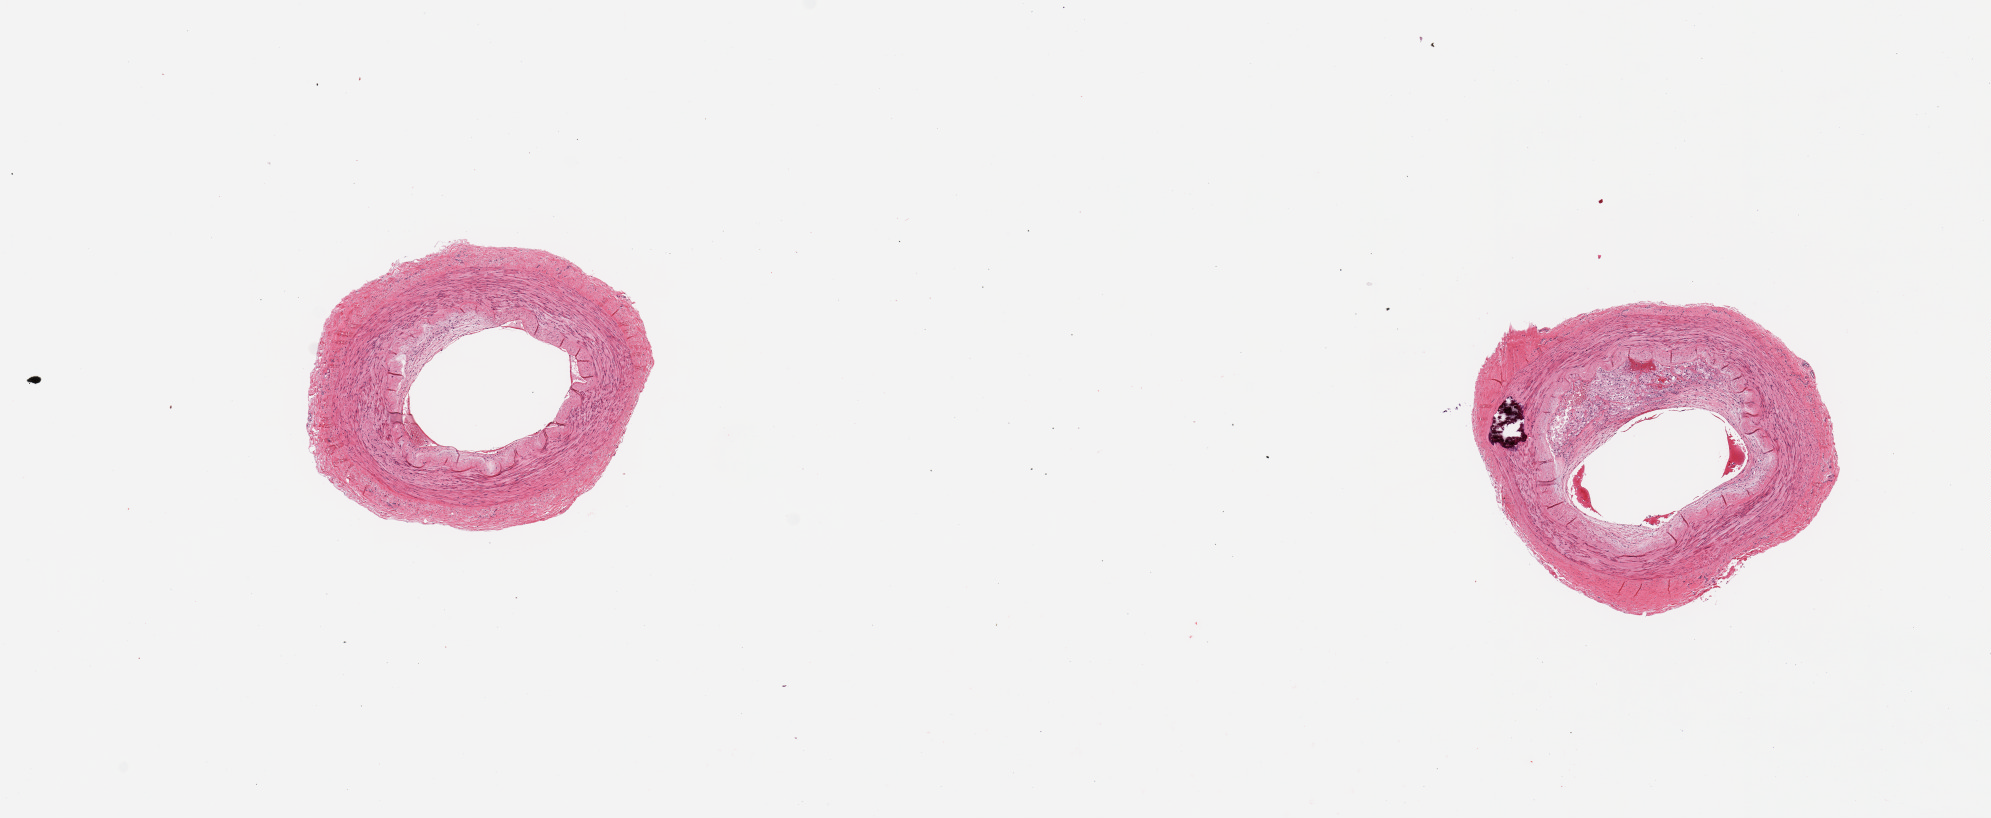
Digitized haematoxylin and eosin-stained section, a low-resolution overview of the entire scanned area, about 15.8 x 6.5 mm (acquisition: 20x scan). PAXgene-fixed, paraffin-embedded tissue. Sampled site (target tissue): tibial artery. Tissue donor sample. Male donor.
- review note (as recorded): 2 pieces, focal Monckeberg sclerosis, ~50% occlusive atherosis up to ~0.4mm thick